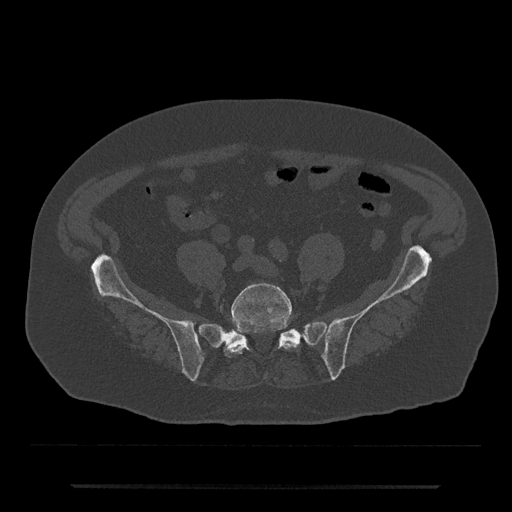
CT including the spine, one axial slice; slice 265 of 797 in the series (ordered by position); reconstruction kernel Br40s/3; 120 kVp; bone window (W 1800 / L 400 HU); 0.5 mm slice thickness; 512 × 512 image matrix. Patient: male, 80 years. From the clinical record (not read from this slice): primary cancer: prostate; vertebrae with lytic lesions (as recorded): L1, T11.
Annotated regions visible in this slice (semi-automatic segmentation, software-assisted and operator-edited):
- L5 vertebra: box from (x=224, y=283) to (x=296, y=357) px